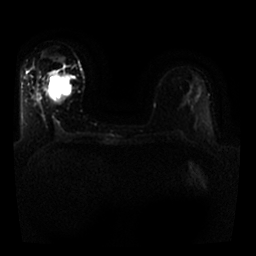
Breast MRI, one axial slice. Position 11 of 25 along the scan axis. Diffusion-weighted series; image 2 of 4 stored at this slice position (different b-values; order by instance number). 1.5 T. 4 mm slice thickness. 256 × 256 image matrix. Female patient.
Structures marked on this image (expert manual segmentation):
- tumour on diffusion-weighted imaging: bounding box [x1, y1, x2, y2] px = [55, 73, 75, 104]